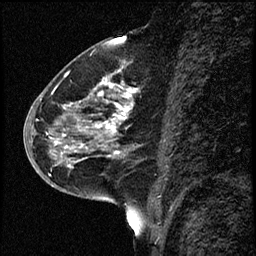
Breast MRI (dynamic contrast-enhanced), one sagittal slice; slice 30 of 68 in the series (ordered by position); dynamic contrast-enhanced study with each time point stored as its own series, time point 2 of 3 at this slice position (early post-contrast, ordered by acquisition time); 1.5 T; TE 4.2 ms, TR 17.6 ms; 2 mm slice thickness; 256 × 256 image matrix, field of view 200 × 200 mm. Female patient, age 52 years. From the clinical record (not read from this slice): setting: breast cancer imaged before/during neoadjuvant chemotherapy; receptor status: HER2-positive.
Outlined on this slice (semi-automatic segmentation, software-assisted and operator-edited):
- analysis volume of interest (the breast-tissue region the enhancement analysis was run in; not a lesion): box from (x=50, y=61) to (x=141, y=184) px
- tumour enhancement mask (voxels above the 100 % enhancement threshold inside the analysis volume of interest): (x=51, y=78)–(x=133, y=167)